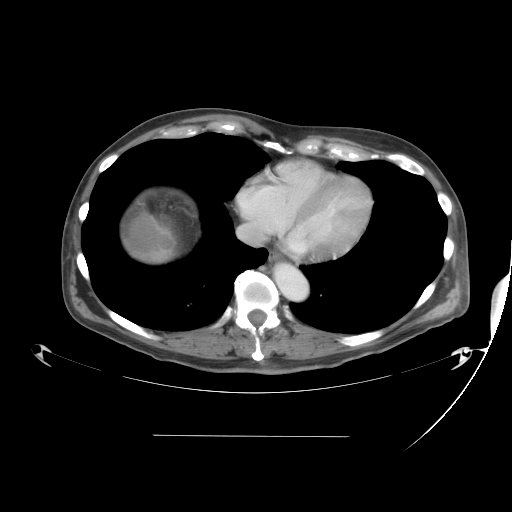
Contrast-enhanced abdominal CT, one axial slice. Slice 42 of 48 in the series (ordered by position). Reconstruction kernel STANDARD. 120 kVp. Soft-tissue window (W 400 / L 40 HU). 512 × 512 image matrix, field of view 486 × 486 mm. Male patient, age 65 years. From the clinical record (not read from this slice): diagnosis: colorectal cancer liver metastases, imaged before liver resection; multiple liver metastases: yes; largest metastasis: 11 cm; chemotherapy before resection: yes.
Annotated regions visible in this slice (manually delineated by an expert):
- liver: bounding box [x1, y1, x2, y2] px = [124, 214, 177, 266]
- liver metastasis: [125, 210, 168, 254]